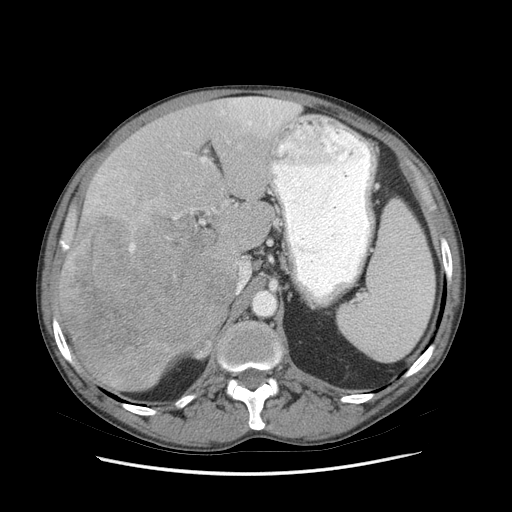
Contrast-enhanced abdominal CT (liver protocol), one axial slice; position 49 of 89 along the scan axis; reconstruction kernel STANDARD; 140 kVp; soft-tissue window (W 400 / L 40 HU); 2.5 mm slice thickness; 512 × 512 image matrix, field of view 380 × 380 mm. Case-level facts recorded for this patient, not image findings: diagnosis: hepatocellular carcinoma (patient treated with transarterial chemoembolisation; whether this scan precedes or follows treatment is not stated here); TNM stage (as recorded): Stage-IIIB.
Outlined on this slice (semi-automatic segmentation, software-assisted and operator-edited):
- liver parenchyma outside the tumour (the mass and vessels are separate outlines, so this box may not span the whole liver): bounding box (x1, y1, x2, y2) in pixels: (56, 96, 299, 390)
- mass: (59, 208, 238, 390)
- liver vessels: (95, 97, 297, 223)